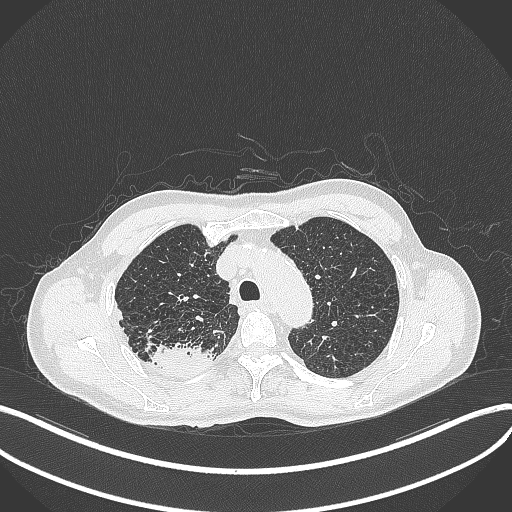
Chest CT, one axial slice; slice 342 of 428 in the series (ordered by position); reconstruction kernel B70f; 120 kVp; lung window (W 1500 / L -600 HU); 512 × 512 image matrix, field of view 400 × 400 mm. Male patient, age 79 years. From the clinical record (not read from this slice): clinical TNM (as recorded): T3 N0 M0.
Outlined on this slice (rectangle marked by the reading radiologist):
- lung tumour (recorded histology: adenocarcinoma): bounding box (x1, y1, x2, y2) in pixels: (147, 340, 213, 377)